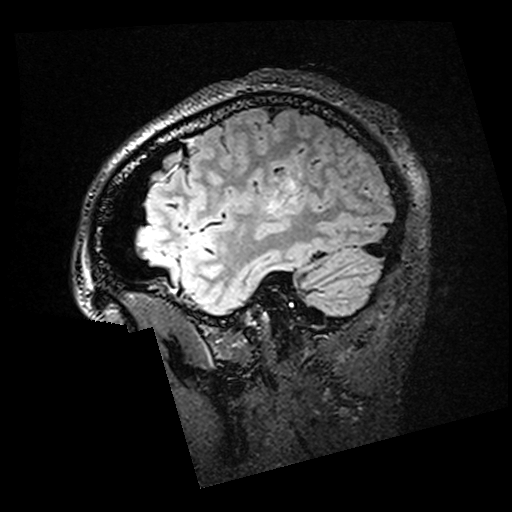
Brain MRI from a brain-tumour surgery series, one sagittal slice. Position 41 of 176 along the scan axis. T2 FLAIR. 1 mm slice thickness. 512 × 512 image matrix, field of view 250 × 250 mm. From the clinical record (not read from this slice): histopathology: Oligodendroglioma; WHO grade: 2.
Outlined on this slice (outlined manually by an expert reader):
- residual tumour: box from (x=295, y=177) to (x=300, y=184) px